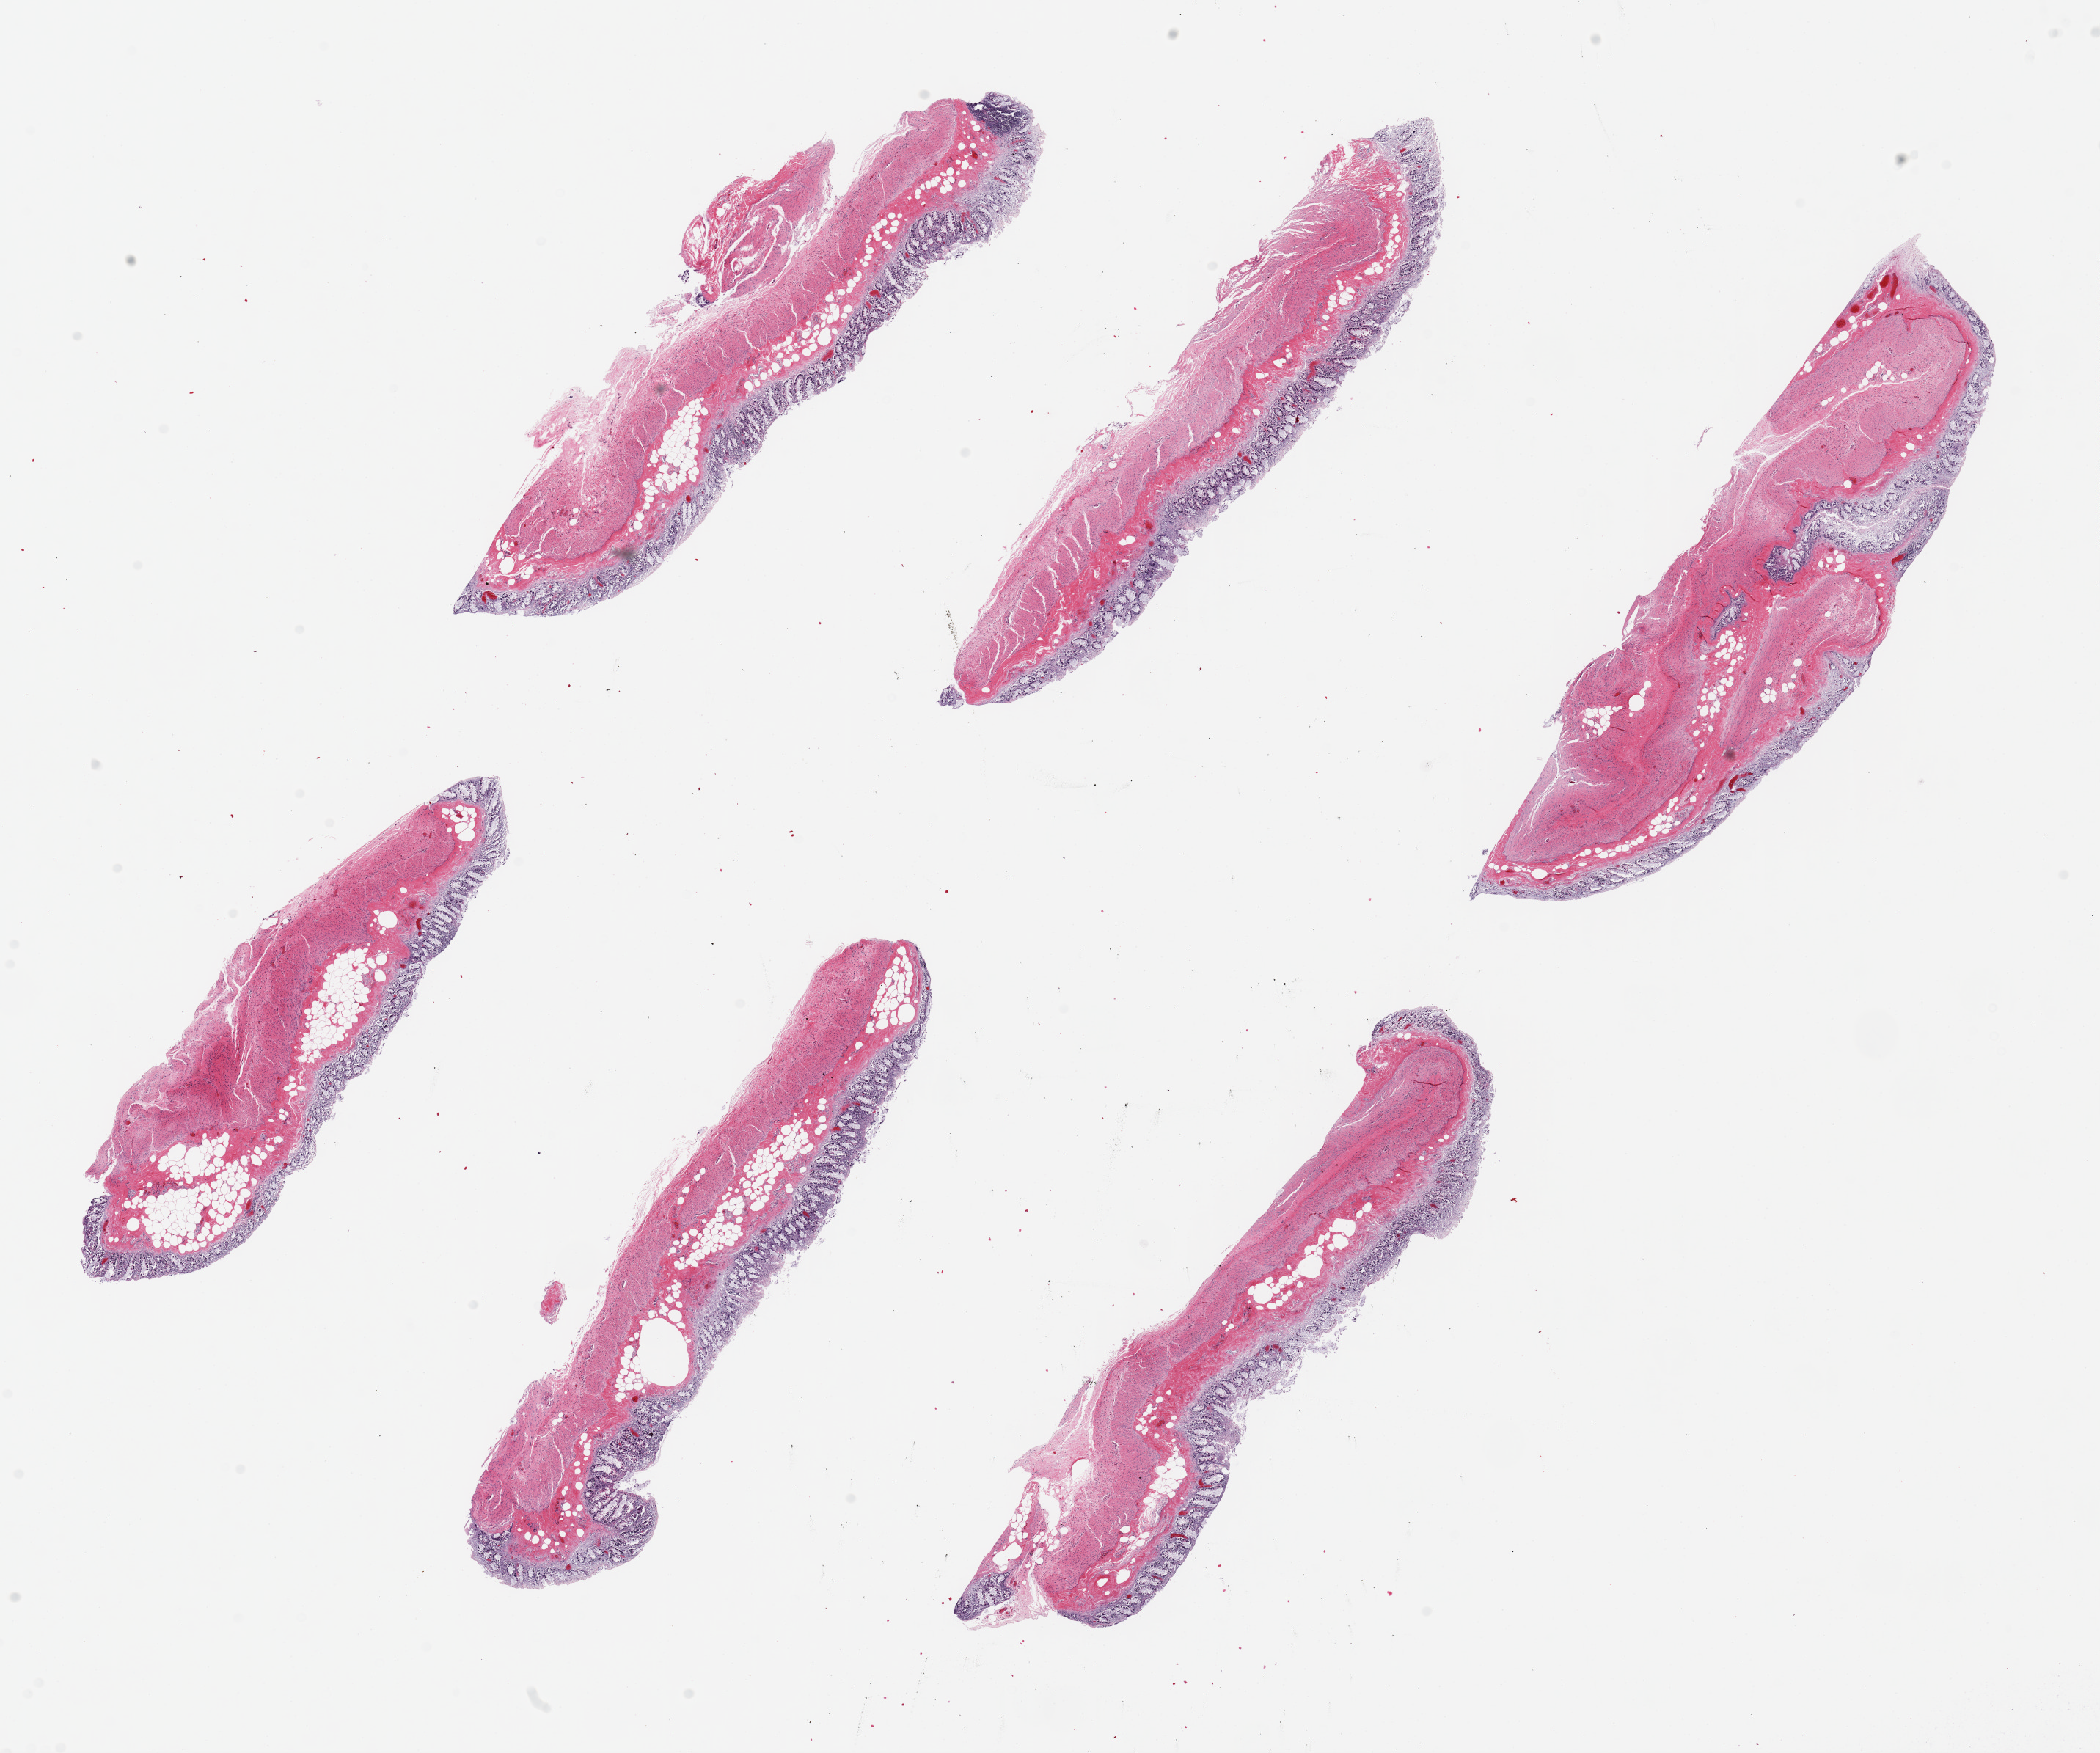
Haematoxylin and eosin whole-slide image — shown as a low-resolution overview of the whole scanned area (about 22.6 x 18.9 mm, acquisition: 20x scan); PAXgene-fixed, paraffin-embedded tissue; target tissue: transverse colon; tissue donor sample. Donor: male.
Pathologist's review note for this sample: 6 pieces, up to 9x3mm; Mucosa badly autolyzed, ~25% of thickness.